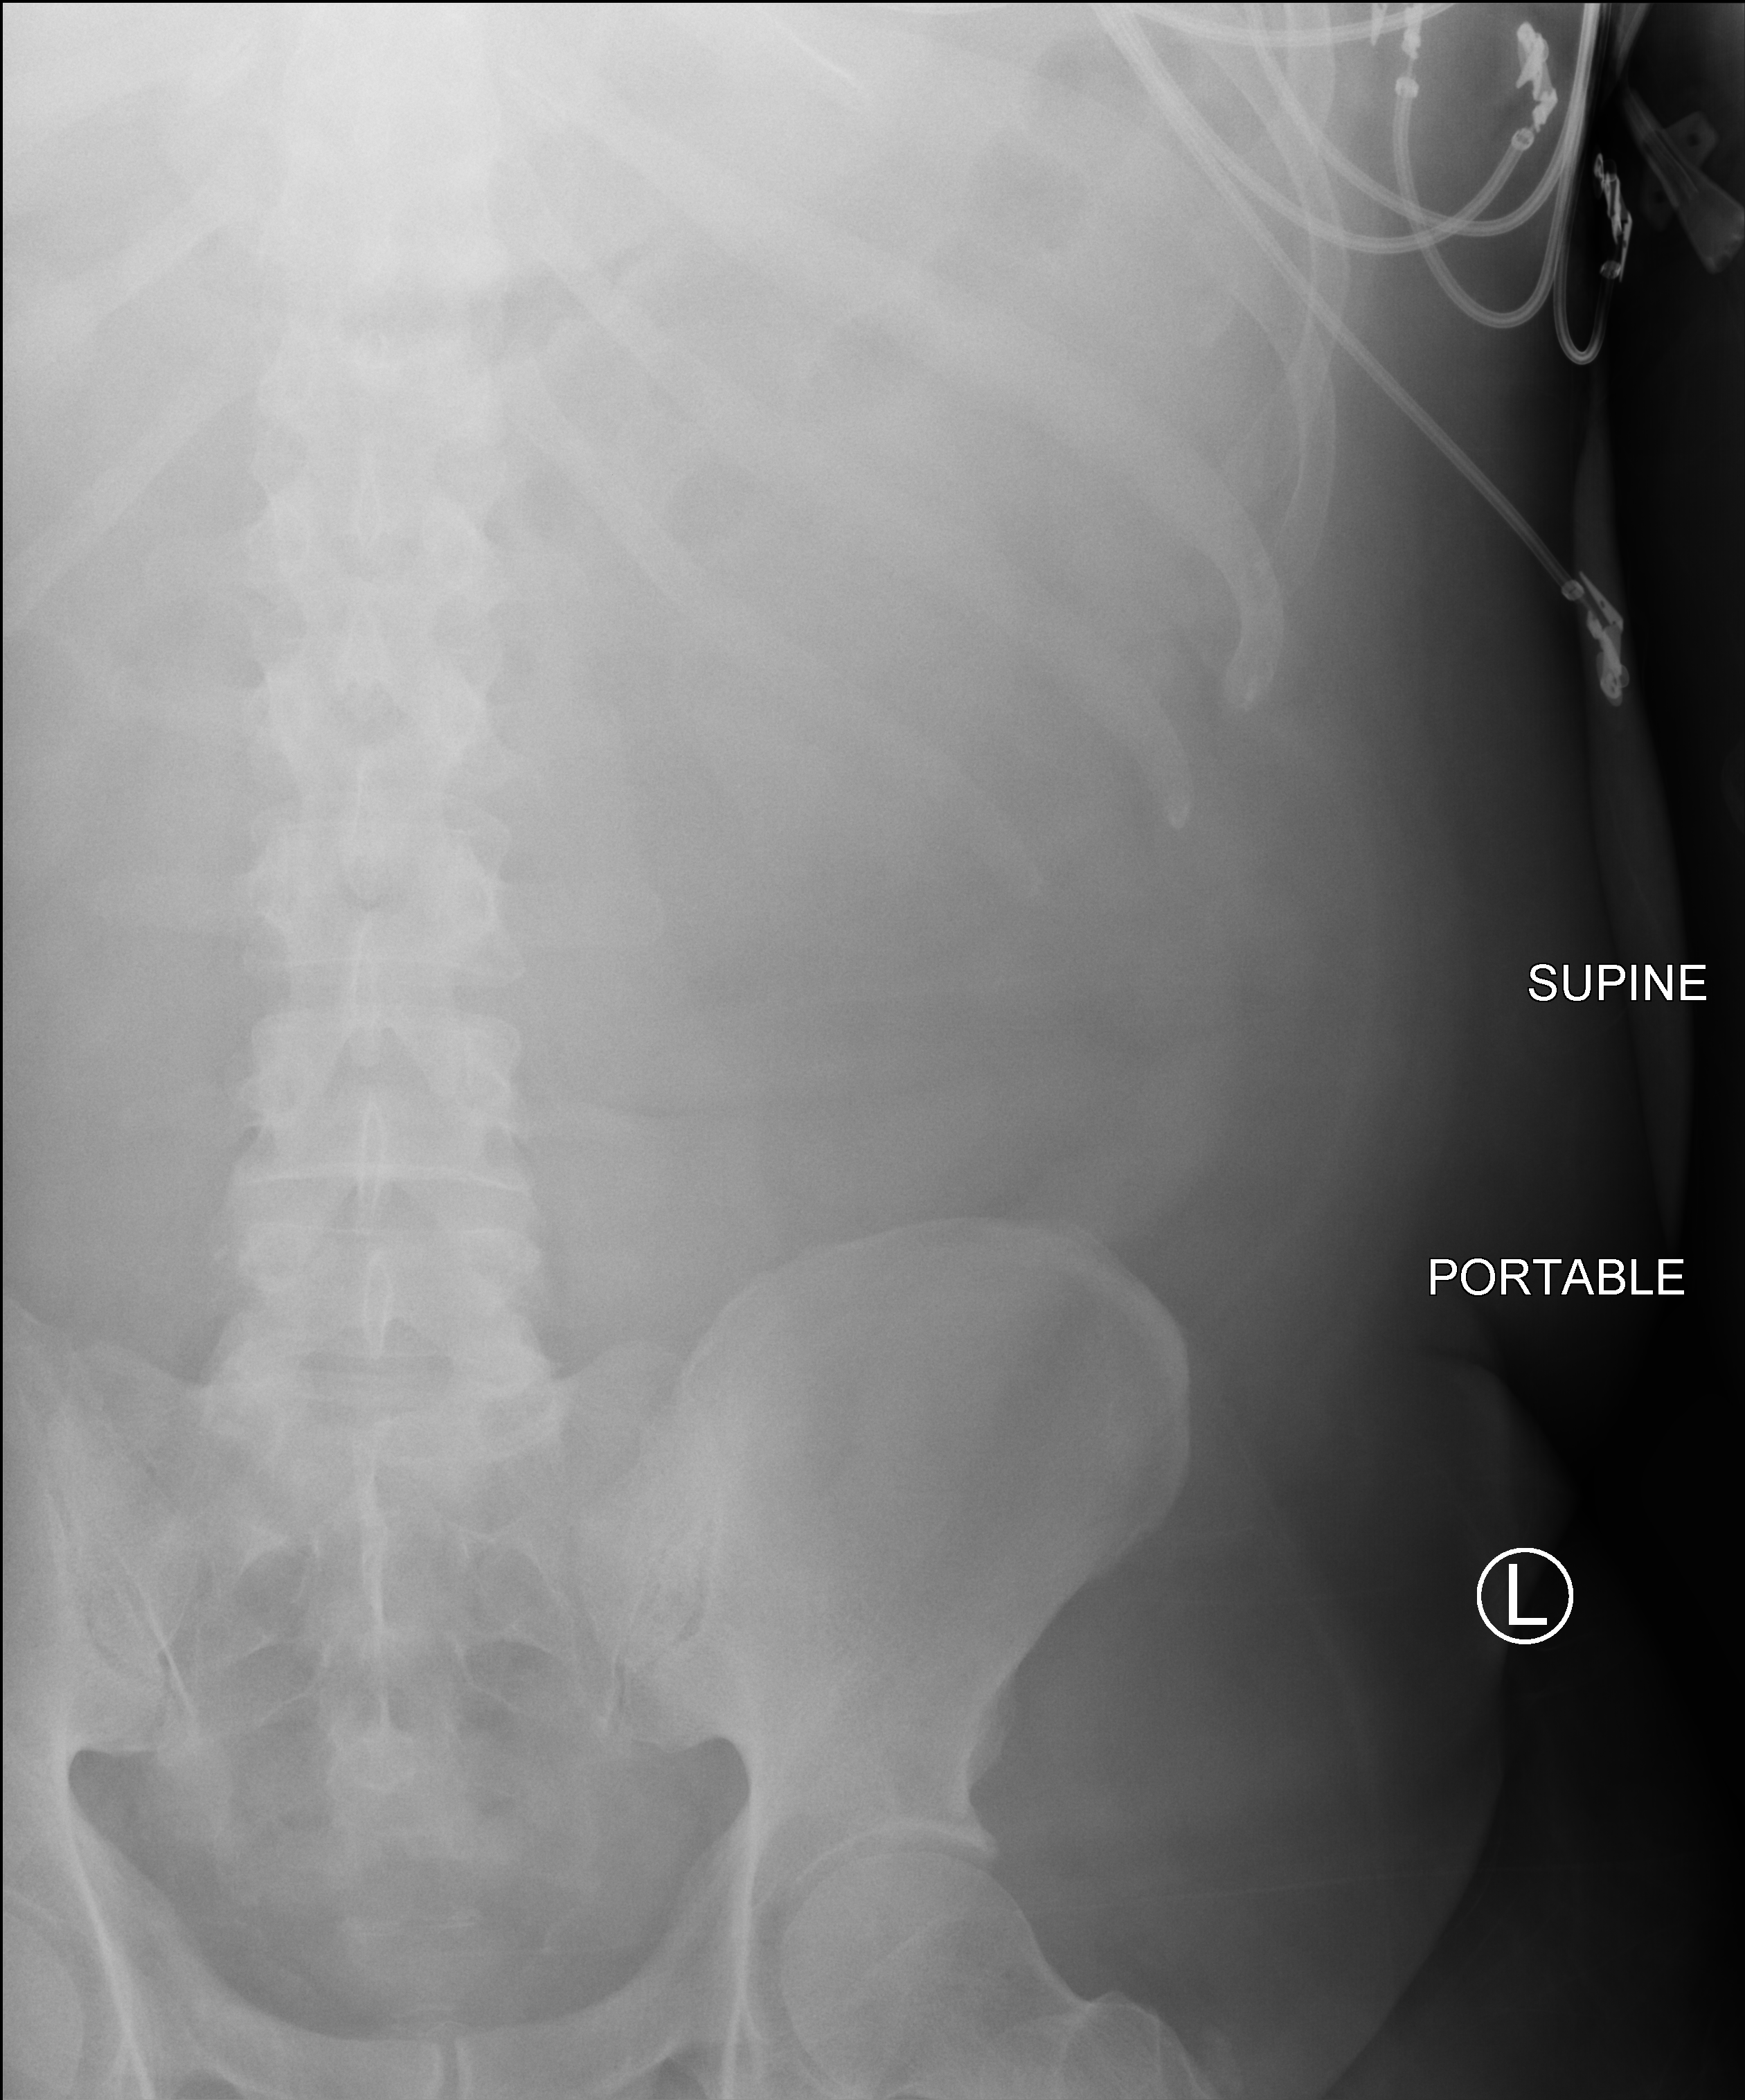
Abdomen X-ray (portable); anteroposterior (AP) projection. Male patient hospitalised with COVID-19, age 18–59 years.
Admission-level facts for this patient (not findings on this image; timing relative to this image not recorded):
- COPD (admission record): no
- chronic kidney disease (admission record): no